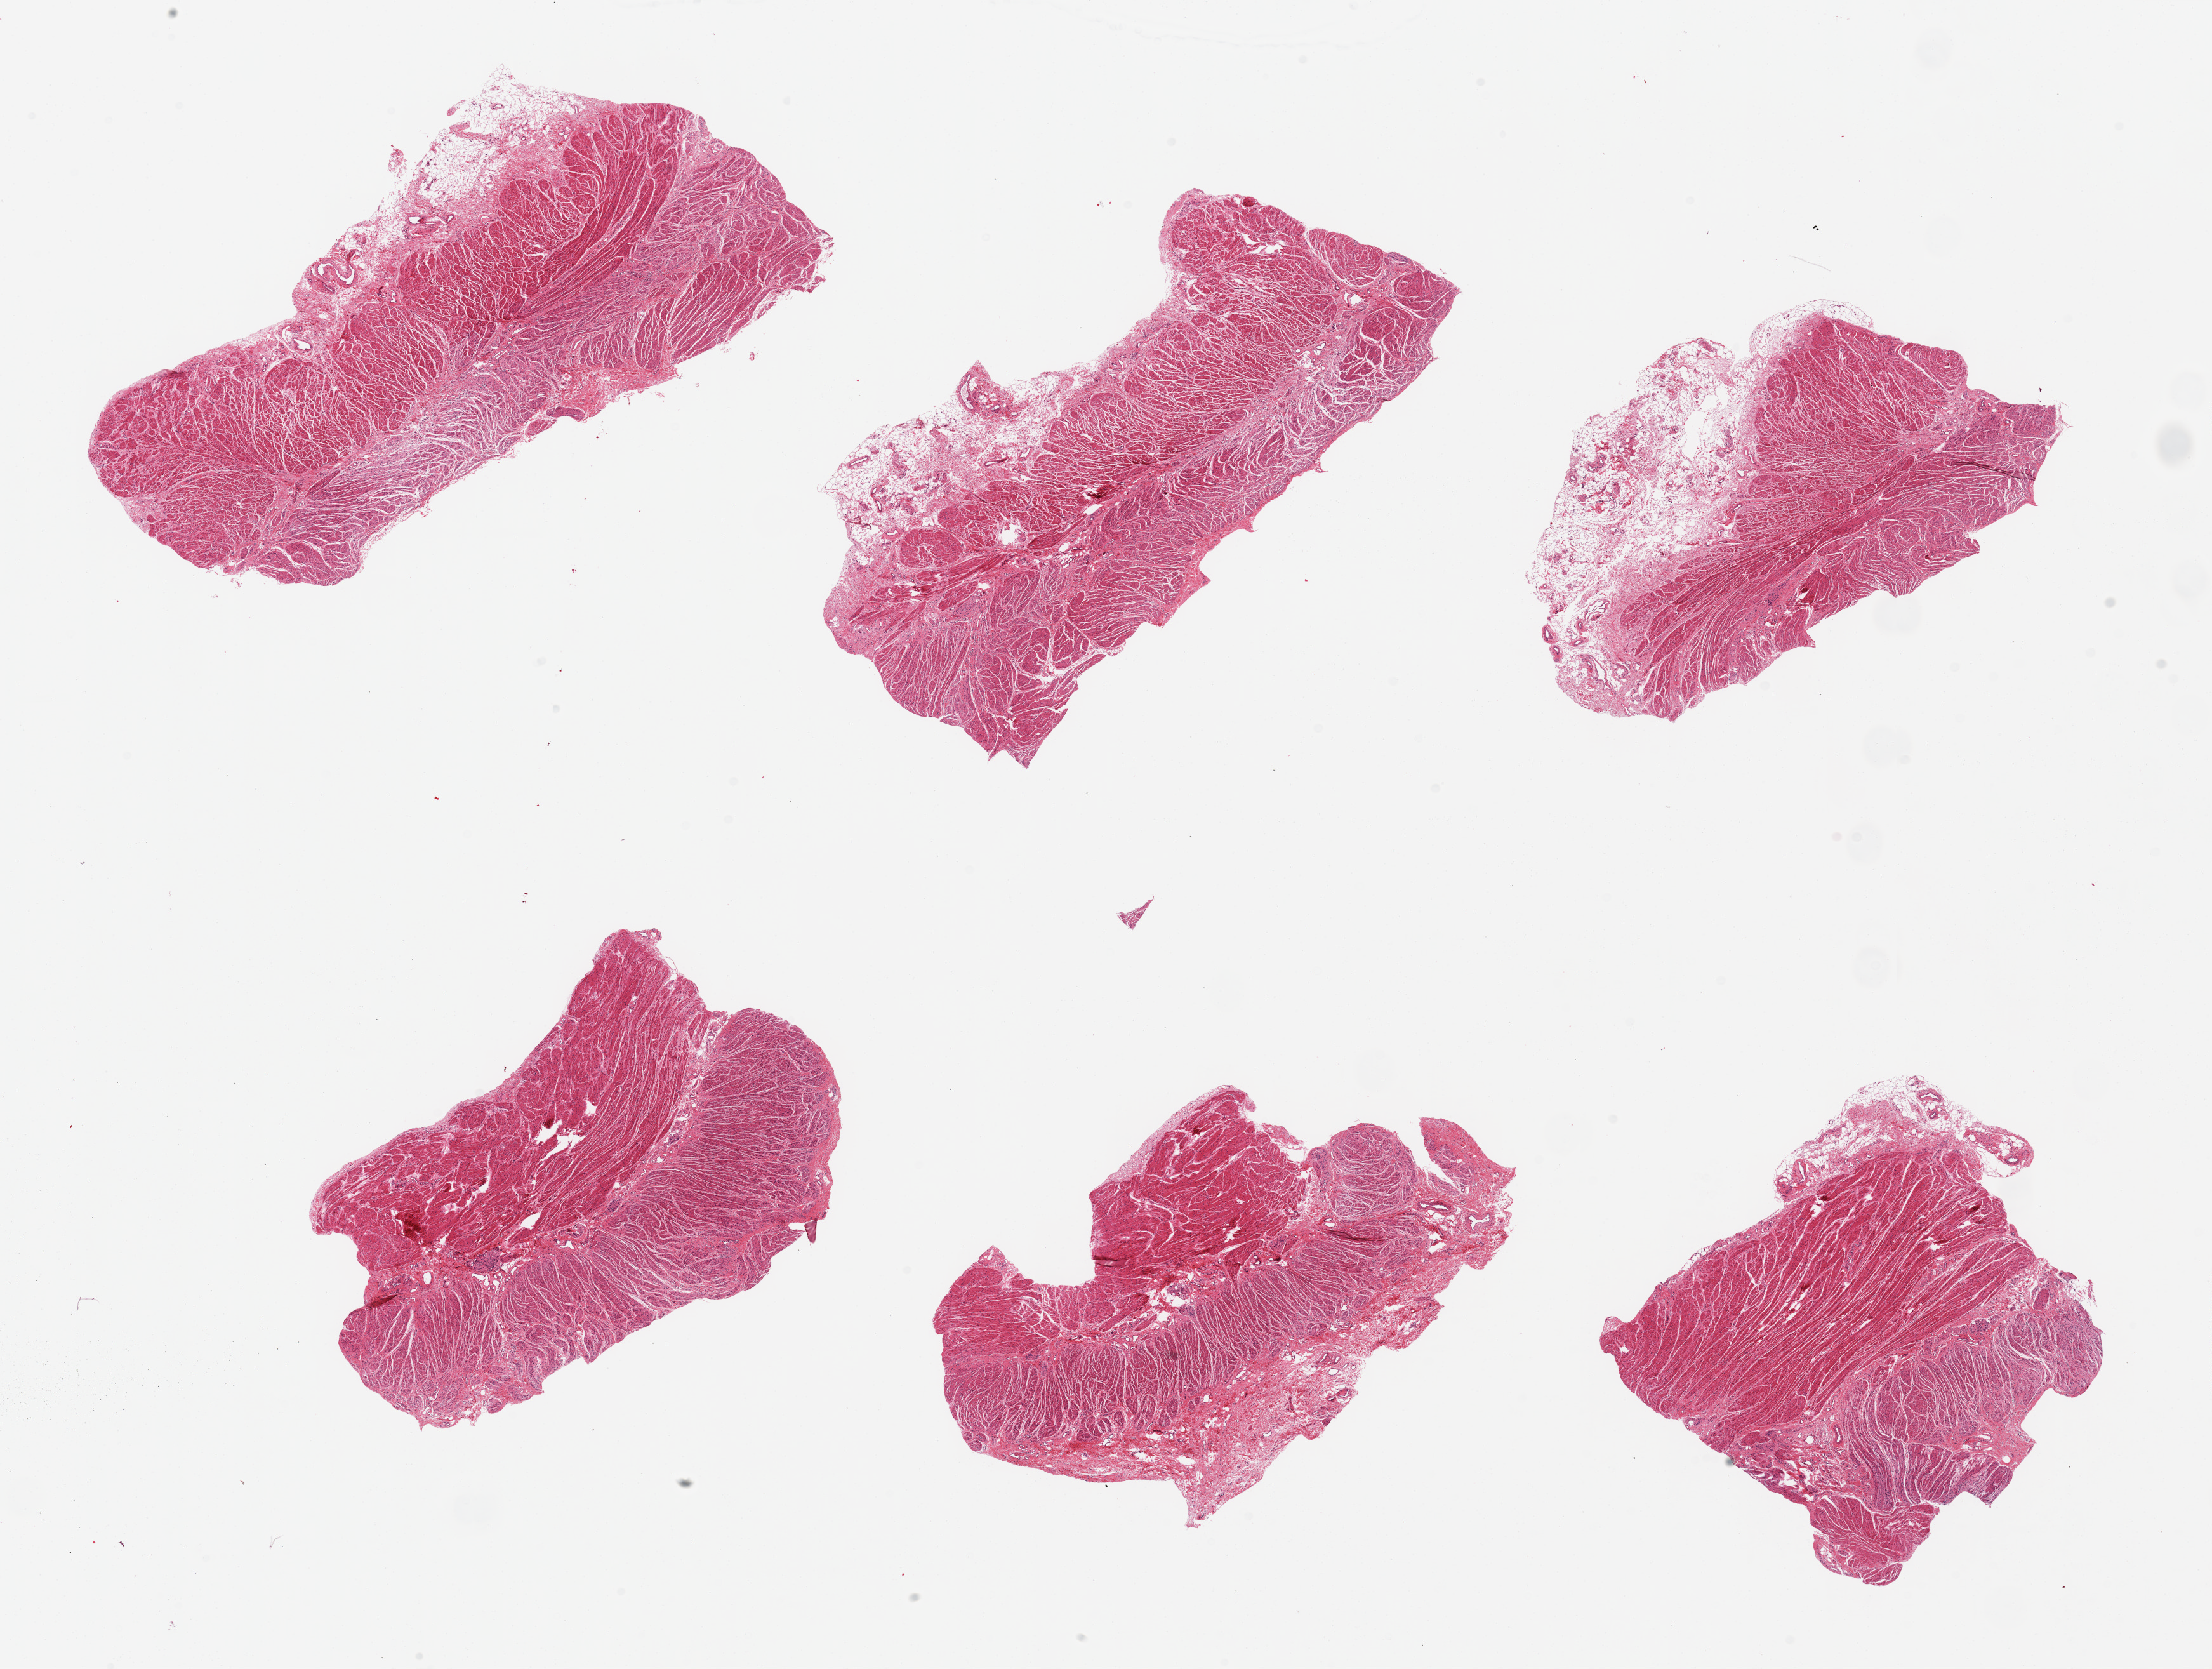
H&E whole-slide image, shown as a low-resolution overview of the whole scanned area (about 27.6 x 20.8 mm). PAXgene-fixed, paraffin-embedded tissue. Target tissue: gastroesophageal junction. Donor tissue sample. Donor sex: female.
Pathologist's review note for this sample: 6 pieces, adherent serosa up to ~2mm on several sections, o/w all muscularis, good specimens.